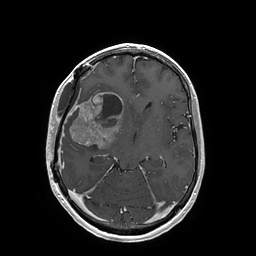
Brain MRI from a brain-tumour surgery series, one axial slice. Position 97 of 202 along the scan axis. T1-weighted post-contrast. 256 × 256 image matrix, field of view 250 × 250 mm. From the clinical record (not read from this slice): histopathology: Glioblastoma; WHO grade: 4; IDH mutation: no; tumour location: Right Insular.
Annotated regions visible in this slice (outlined manually by an expert reader):
- tumour: box from (x=69, y=92) to (x=122, y=149) px